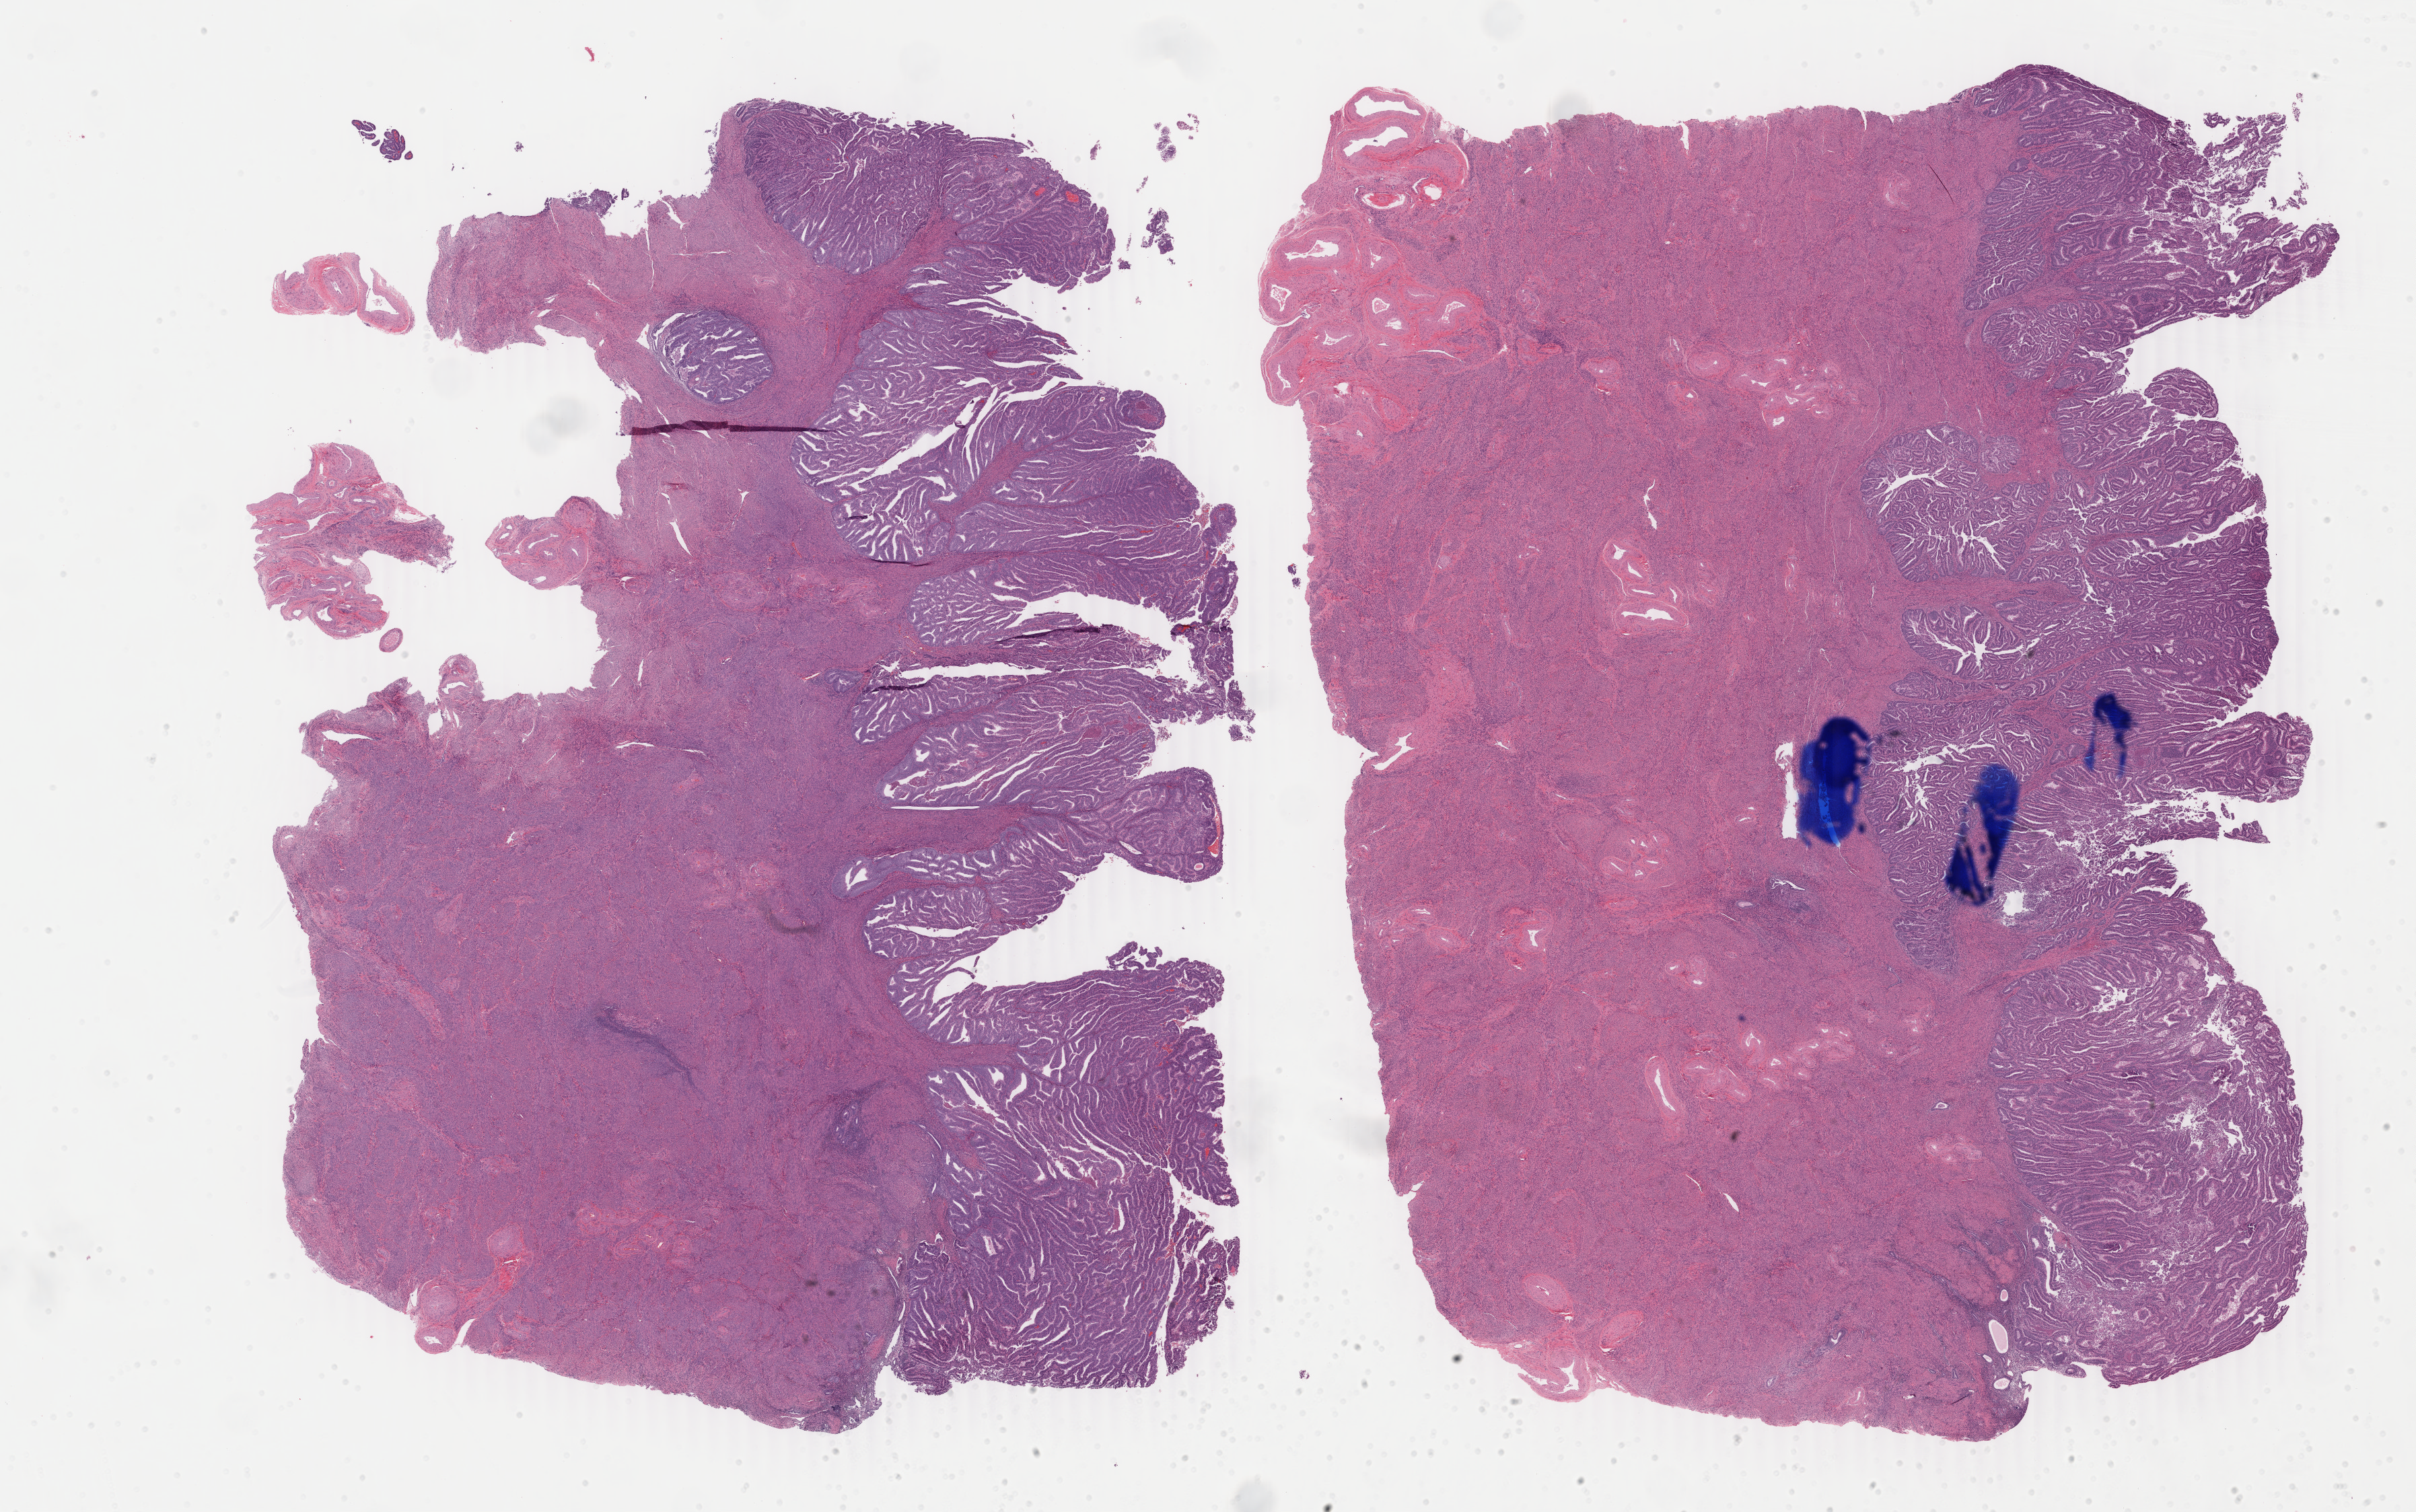
Digitized Hematoxylin and eosin (H&E) stained tissue section (whole slide), whole scanned area (about 28.6 x 17.9 mm, from a 40x scan) shown as a low-resolution overview; formalin-fixed paraffin-embedded (FFPE) diagnostic section; uterus, primary tumour sample. Patient: female, age at initial diagnosis 57 years. Histologic grade: G2 (moderately differentiated).
FIGO stage: IB. Lymph nodes positive (case pathology): 0 of 48 examined. Histologic diagnosis: Endometrioid adenocarcinoma, NOS.